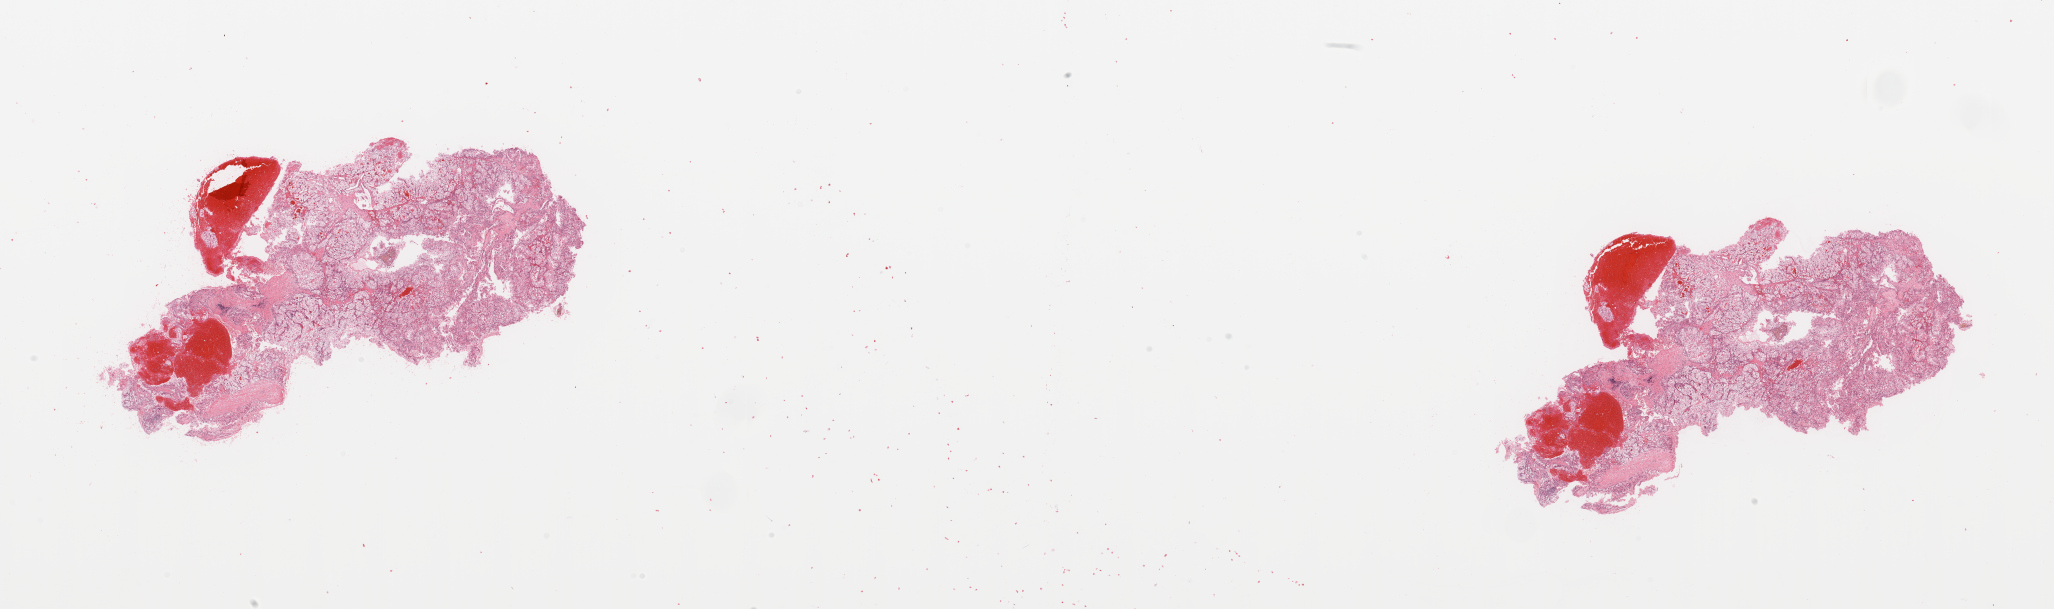
Whole-slide histology image, Hematoxylin and eosin (H&E) stained, a low-resolution overview of the entire scanned area, about 32.5 x 9.6 mm (acquisition: 20x scan). Kidney, tumour tissue. Male, 54 y/o. Histologic grade: G2 (moderately differentiated).
* primary tumour site (as recorded): middle
* AJCC pathologic stage: I
* diagnosis: Renal cell carcinoma, NOS